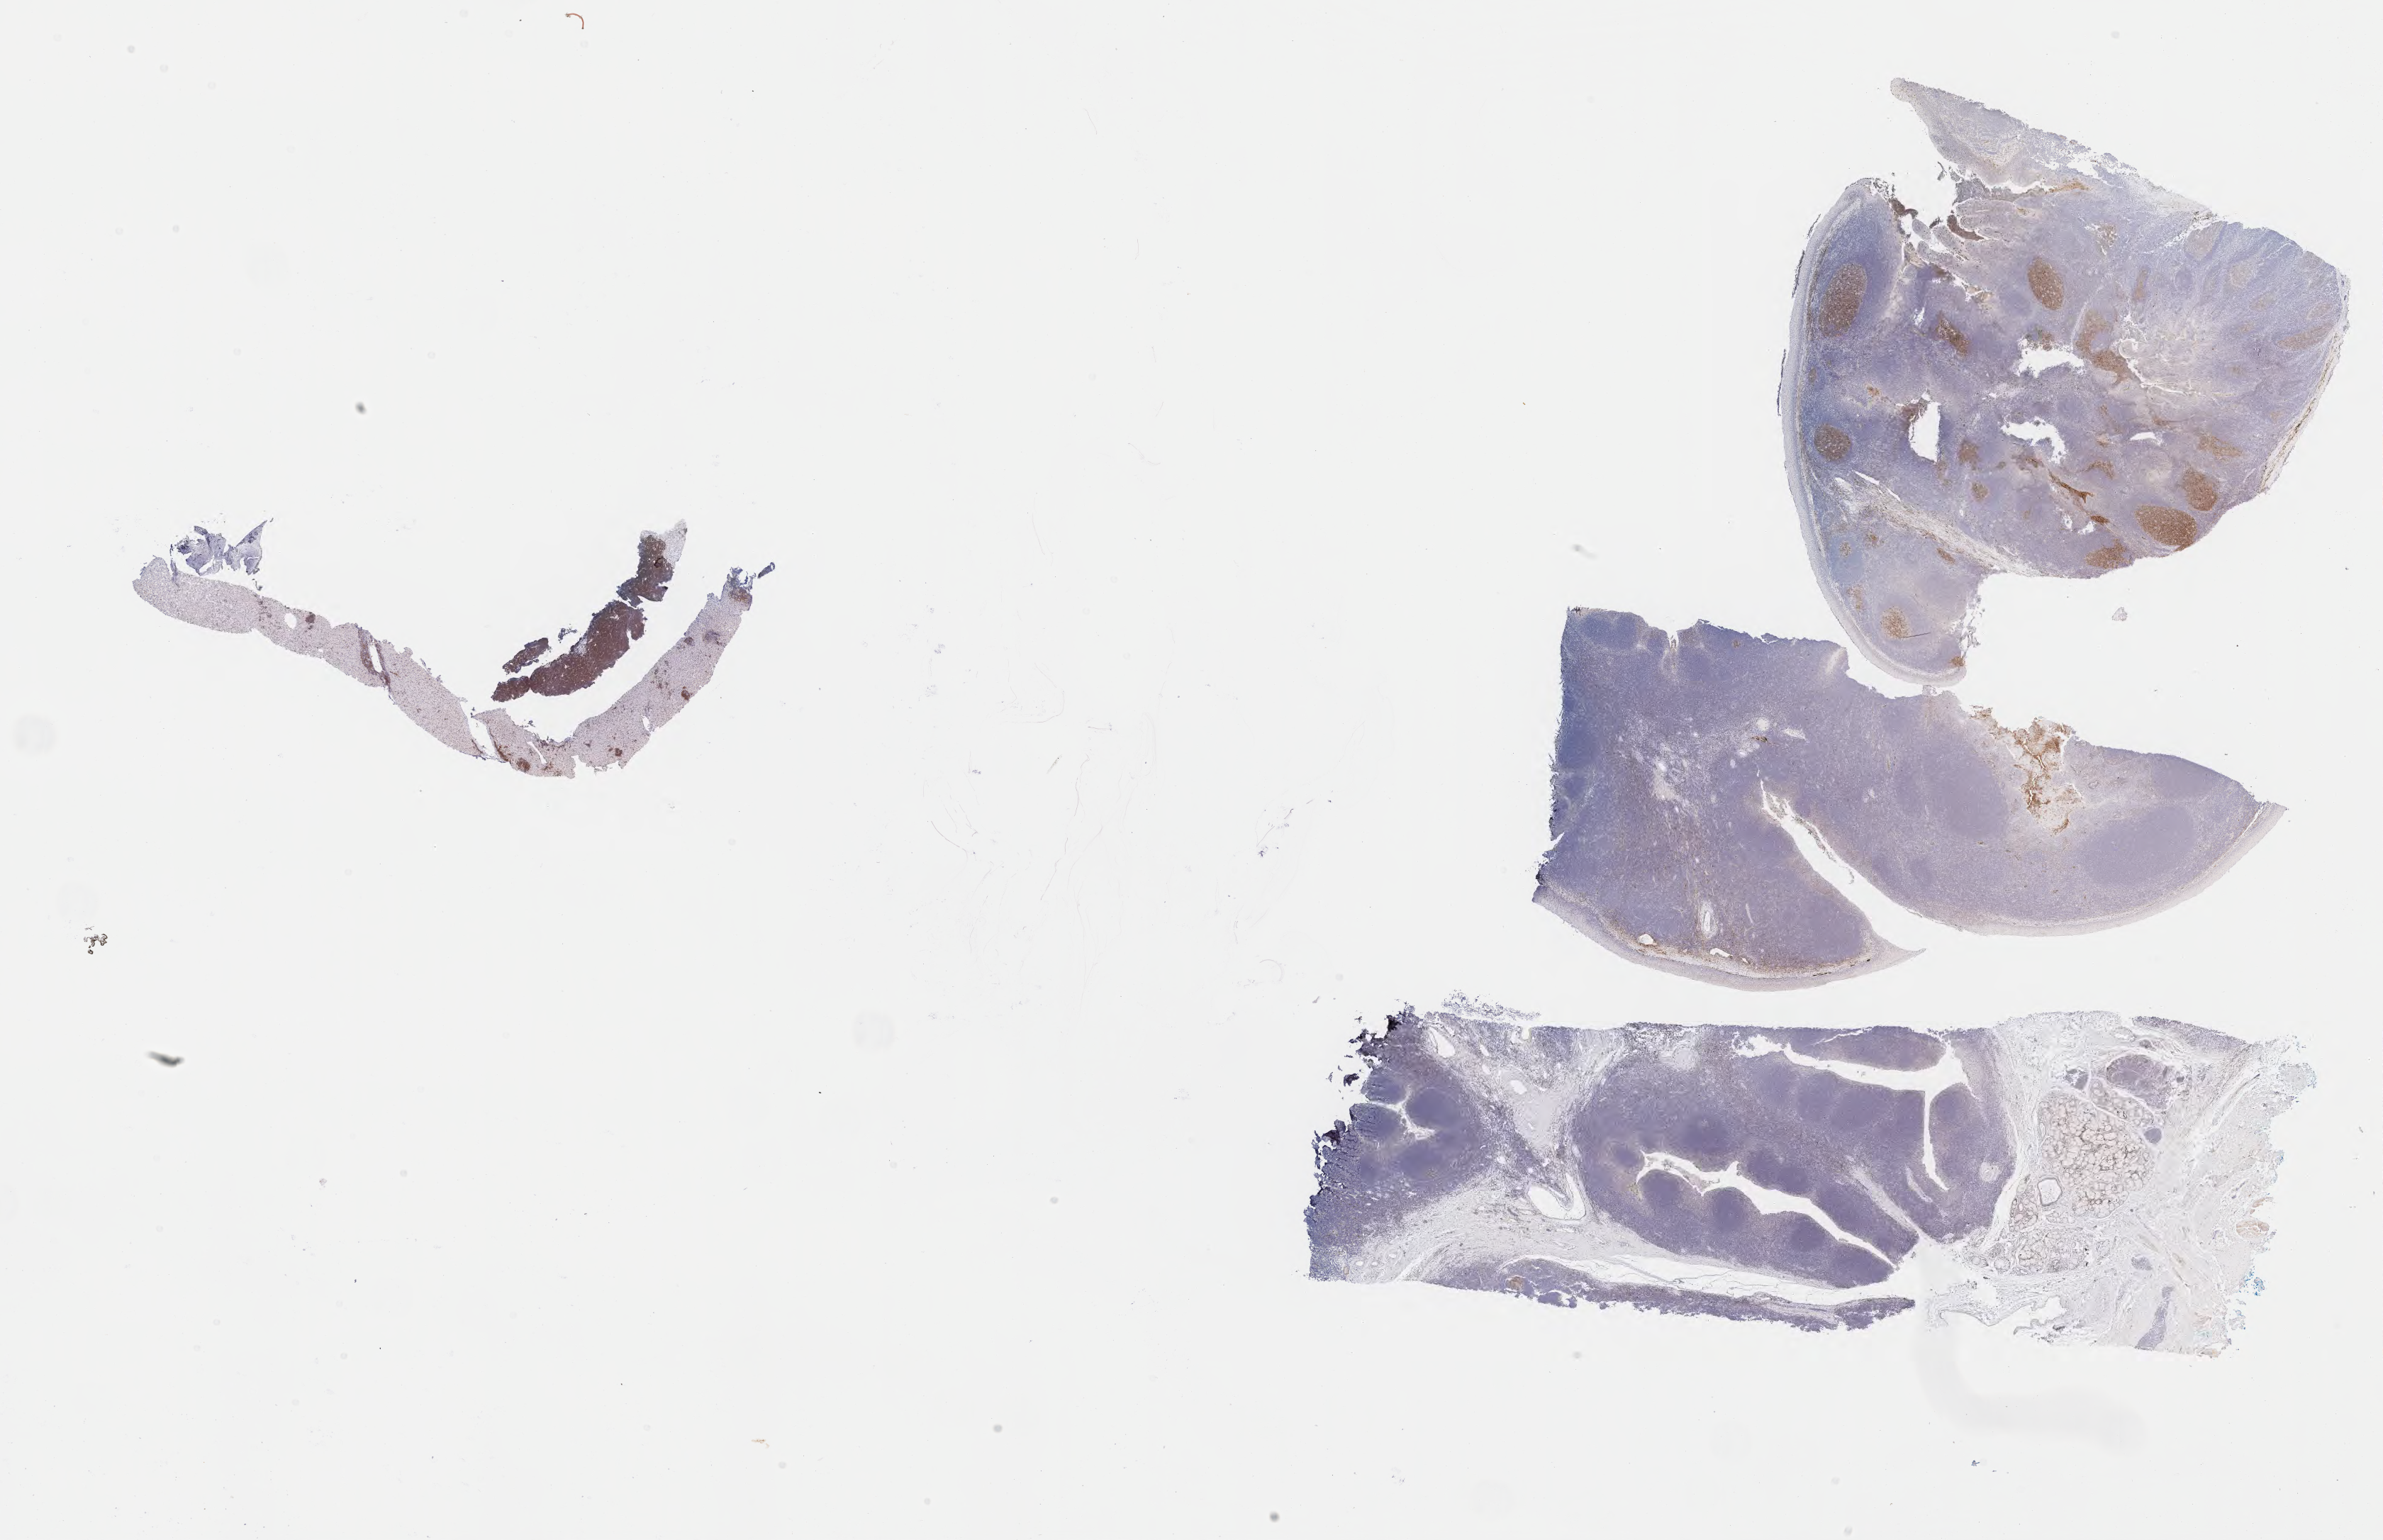
IHC for CD10, whole-slide image — whole scanned area (about 27.2 x 17.6 mm) shown as a low-resolution overview, specimen: tumor tissue, site: liver. Patient: male, age at initial diagnosis 7 years.
• diagnosis: Burkitt lymphoma, NOS